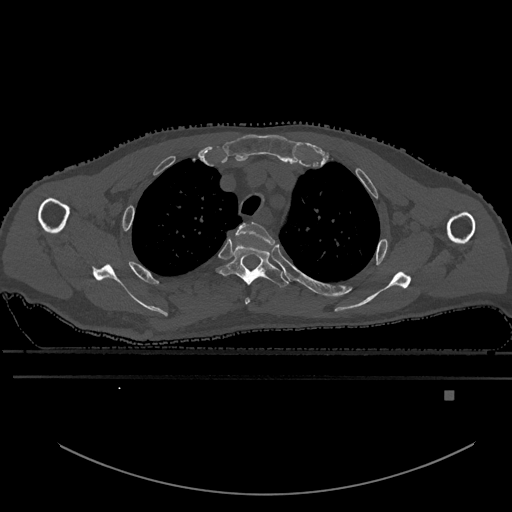
CT including the spine, one axial slice; bone window (W 1800 / L 400 HU); 512 × 512 image matrix, field of view 456 × 456 mm. Patient: male, 82 years. Case-level facts recorded for this patient, not image findings: primary cancer: prostate.
Annotated regions visible in this slice (semi-automatically segmented with operator editing):
- T2 vertebra: bounding box [x1, y1, x2, y2] px = [235, 221, 275, 305]
- T3 vertebra: [217, 242, 289, 287]